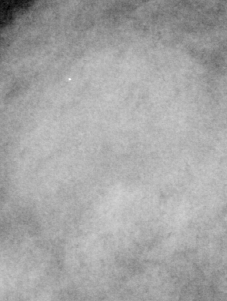
Region of interest cut from a scanned film mammogram (one marked finding), right breast, CC view, BI-RADS breast density category 3 (scale 1–4).
Finding: mass, shape oval, margins microlobulated; BI-RADS assessment category 4; subtlety rating 4 on a 1 (subtle) to 5 (obvious) scale; pathology (as recorded): benign.